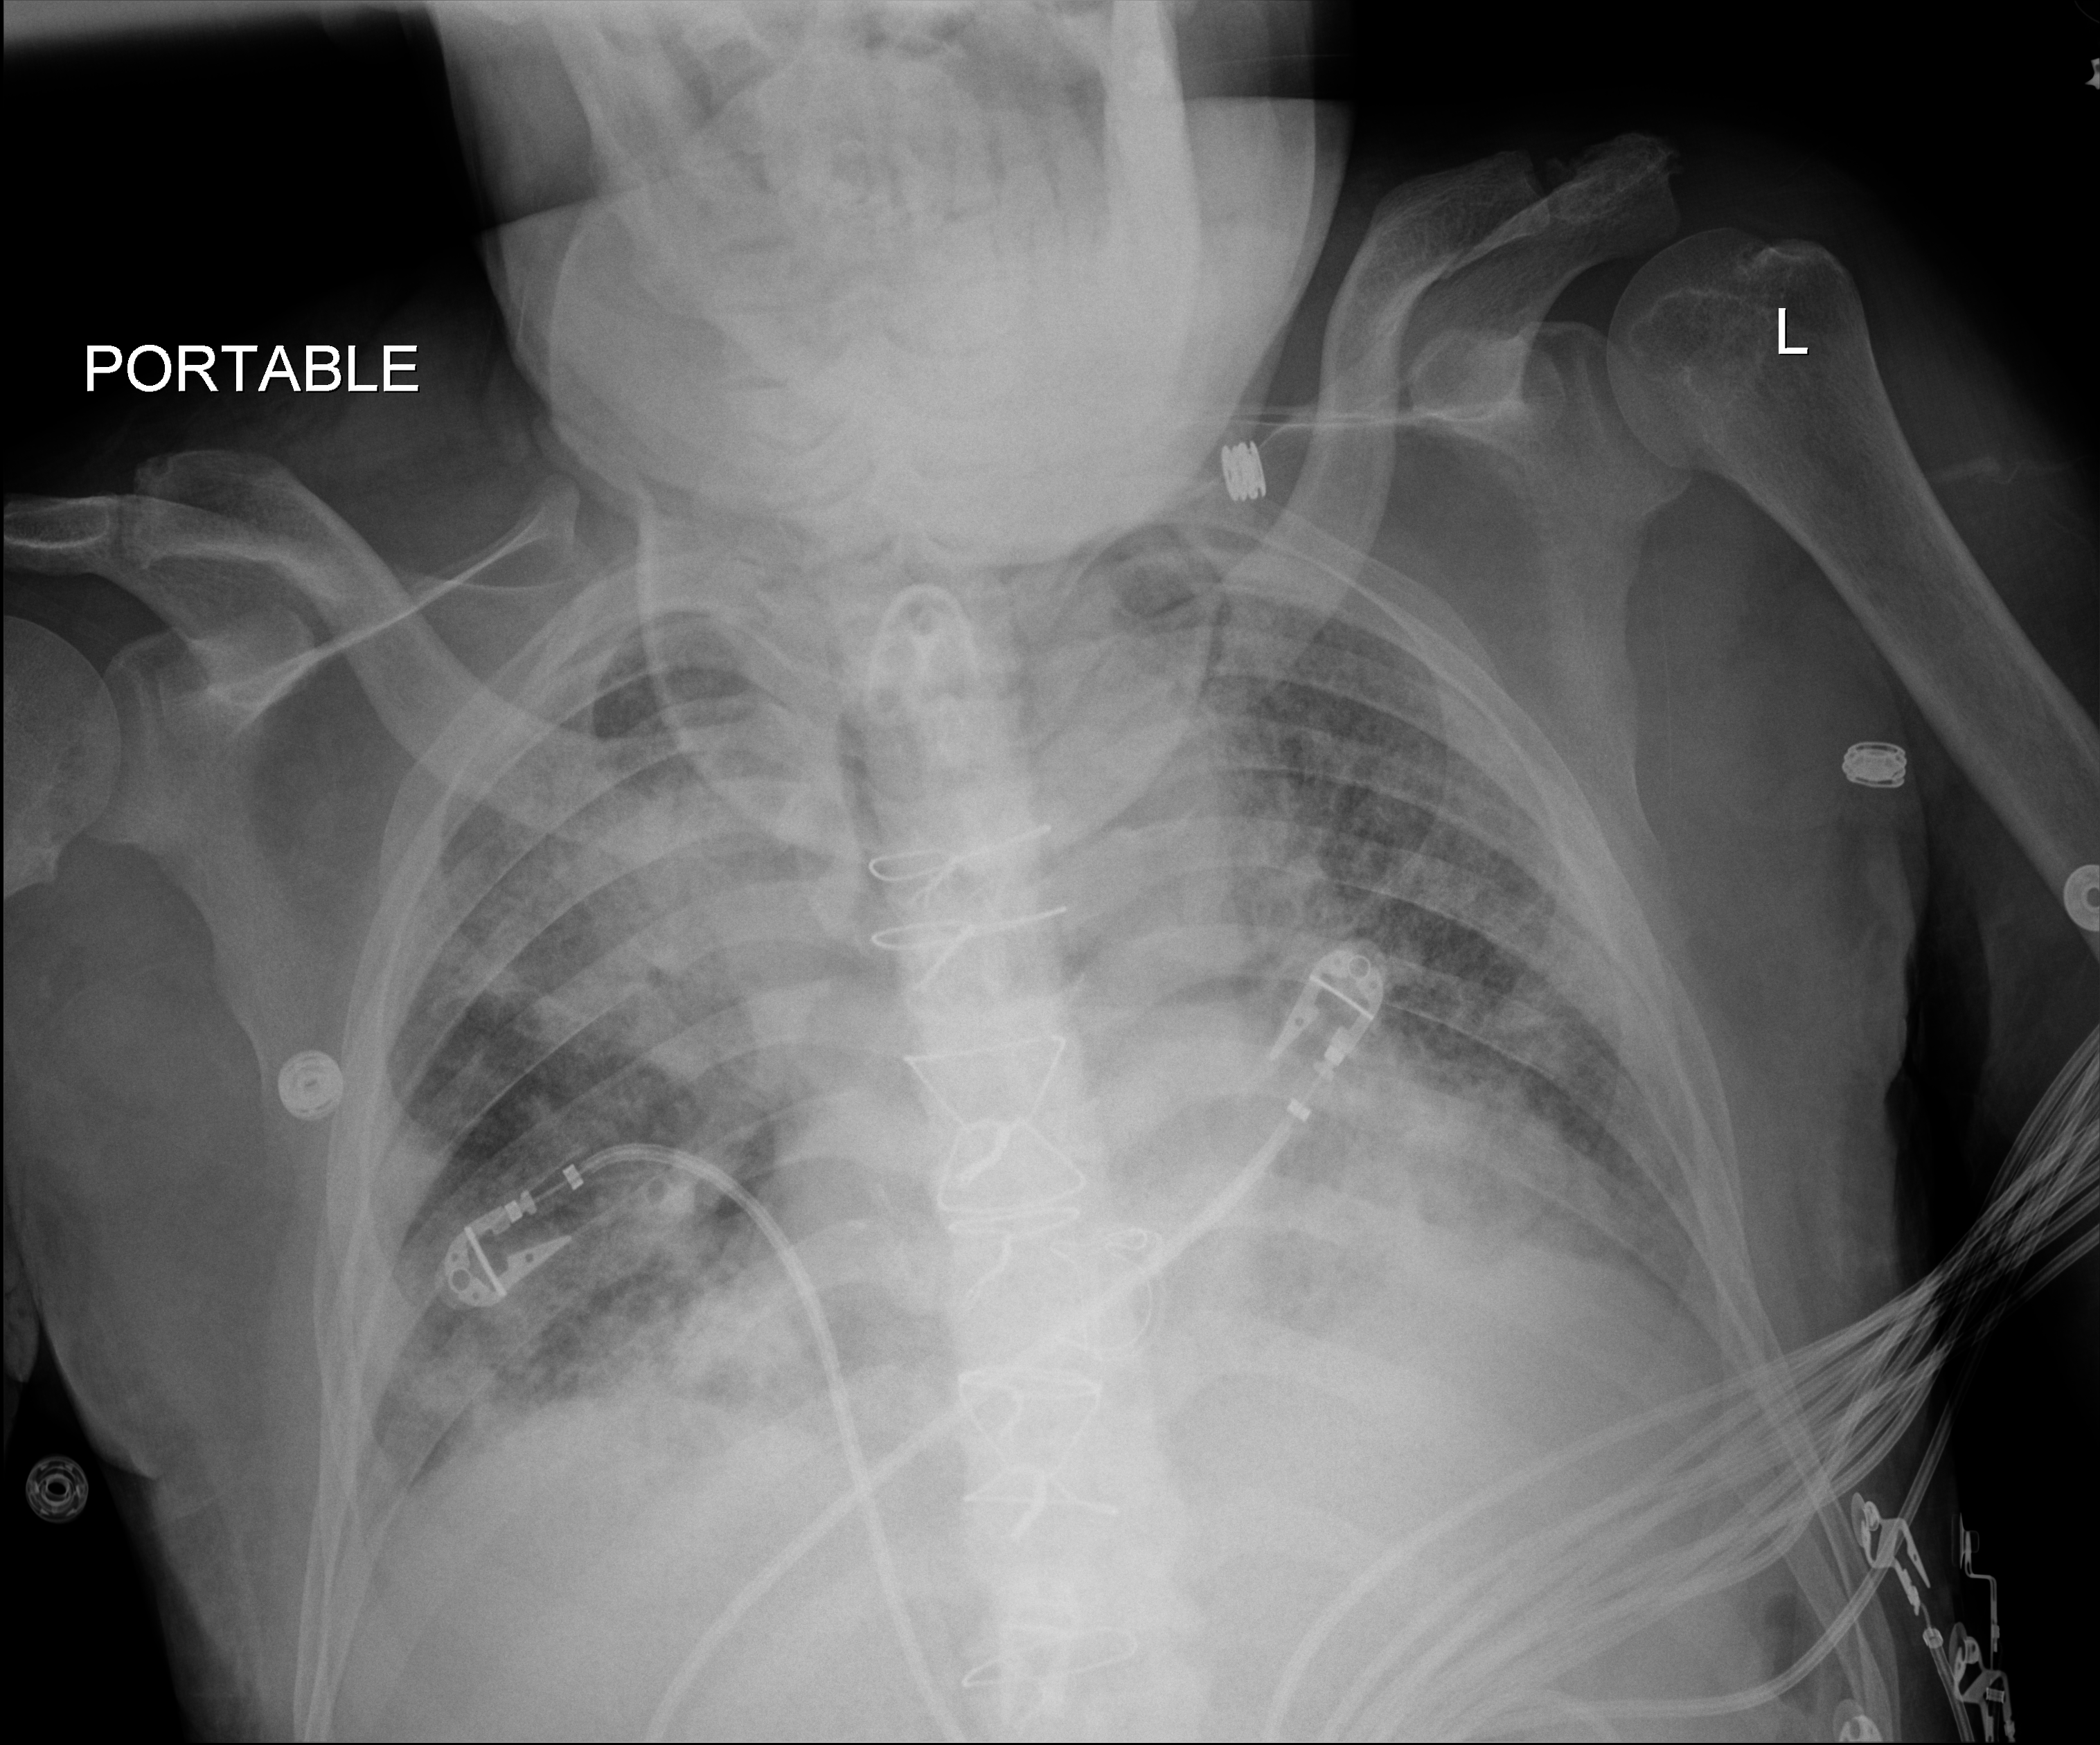
Portable chest radiograph, anteroposterior (AP) projection. Patient hospitalised with COVID-19; male, aged 60–74 years.
From the hospital-stay record, not from the radiograph (when in the stay this image was taken is not recorded): admitted to intensive care during this hospital stay: yes.